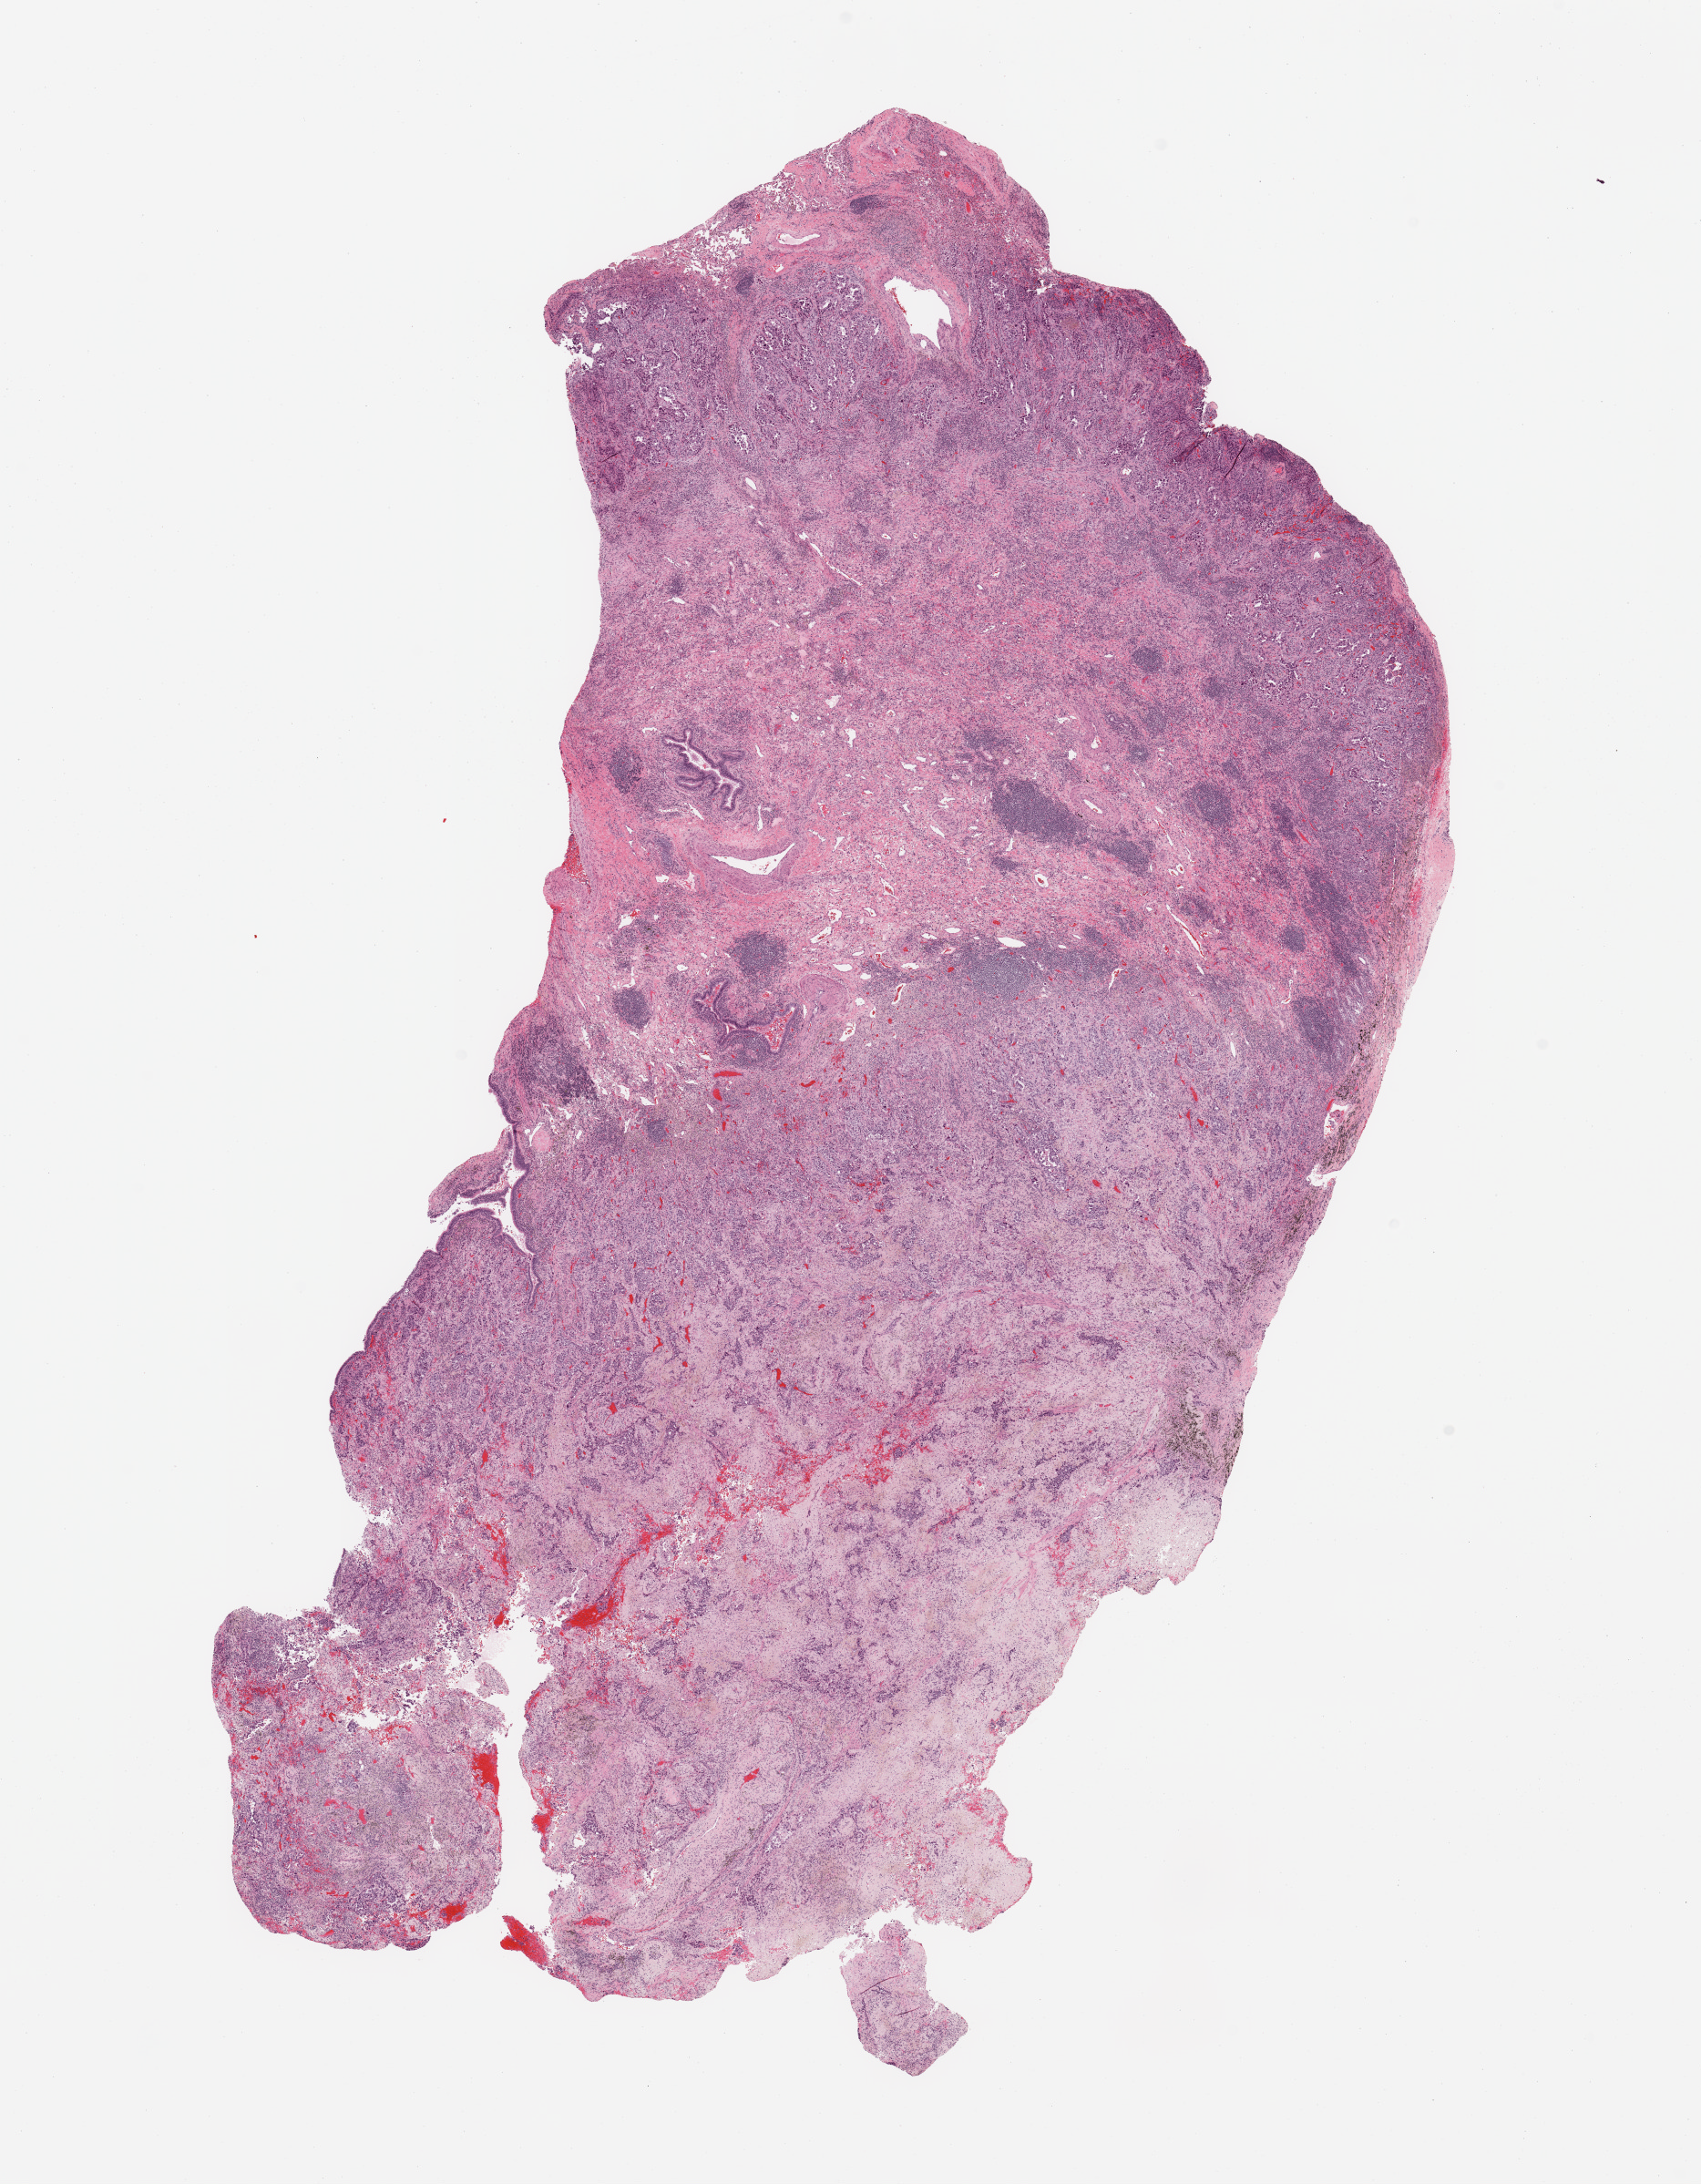
Whole-slide histology image, H&E, shown as a low-resolution overview of the whole scanned area (about 14.8 x 19.0 mm, slide scanned at 20x). Tumour tissue sample, lung. Female, 56 y/o. Histologic grade: G2 (moderately differentiated).
Primary tumour site (as recorded): left upper lobe. Histologic diagnosis: Adenocarcinoma, NOS. AJCC pathologic stage: IIB.